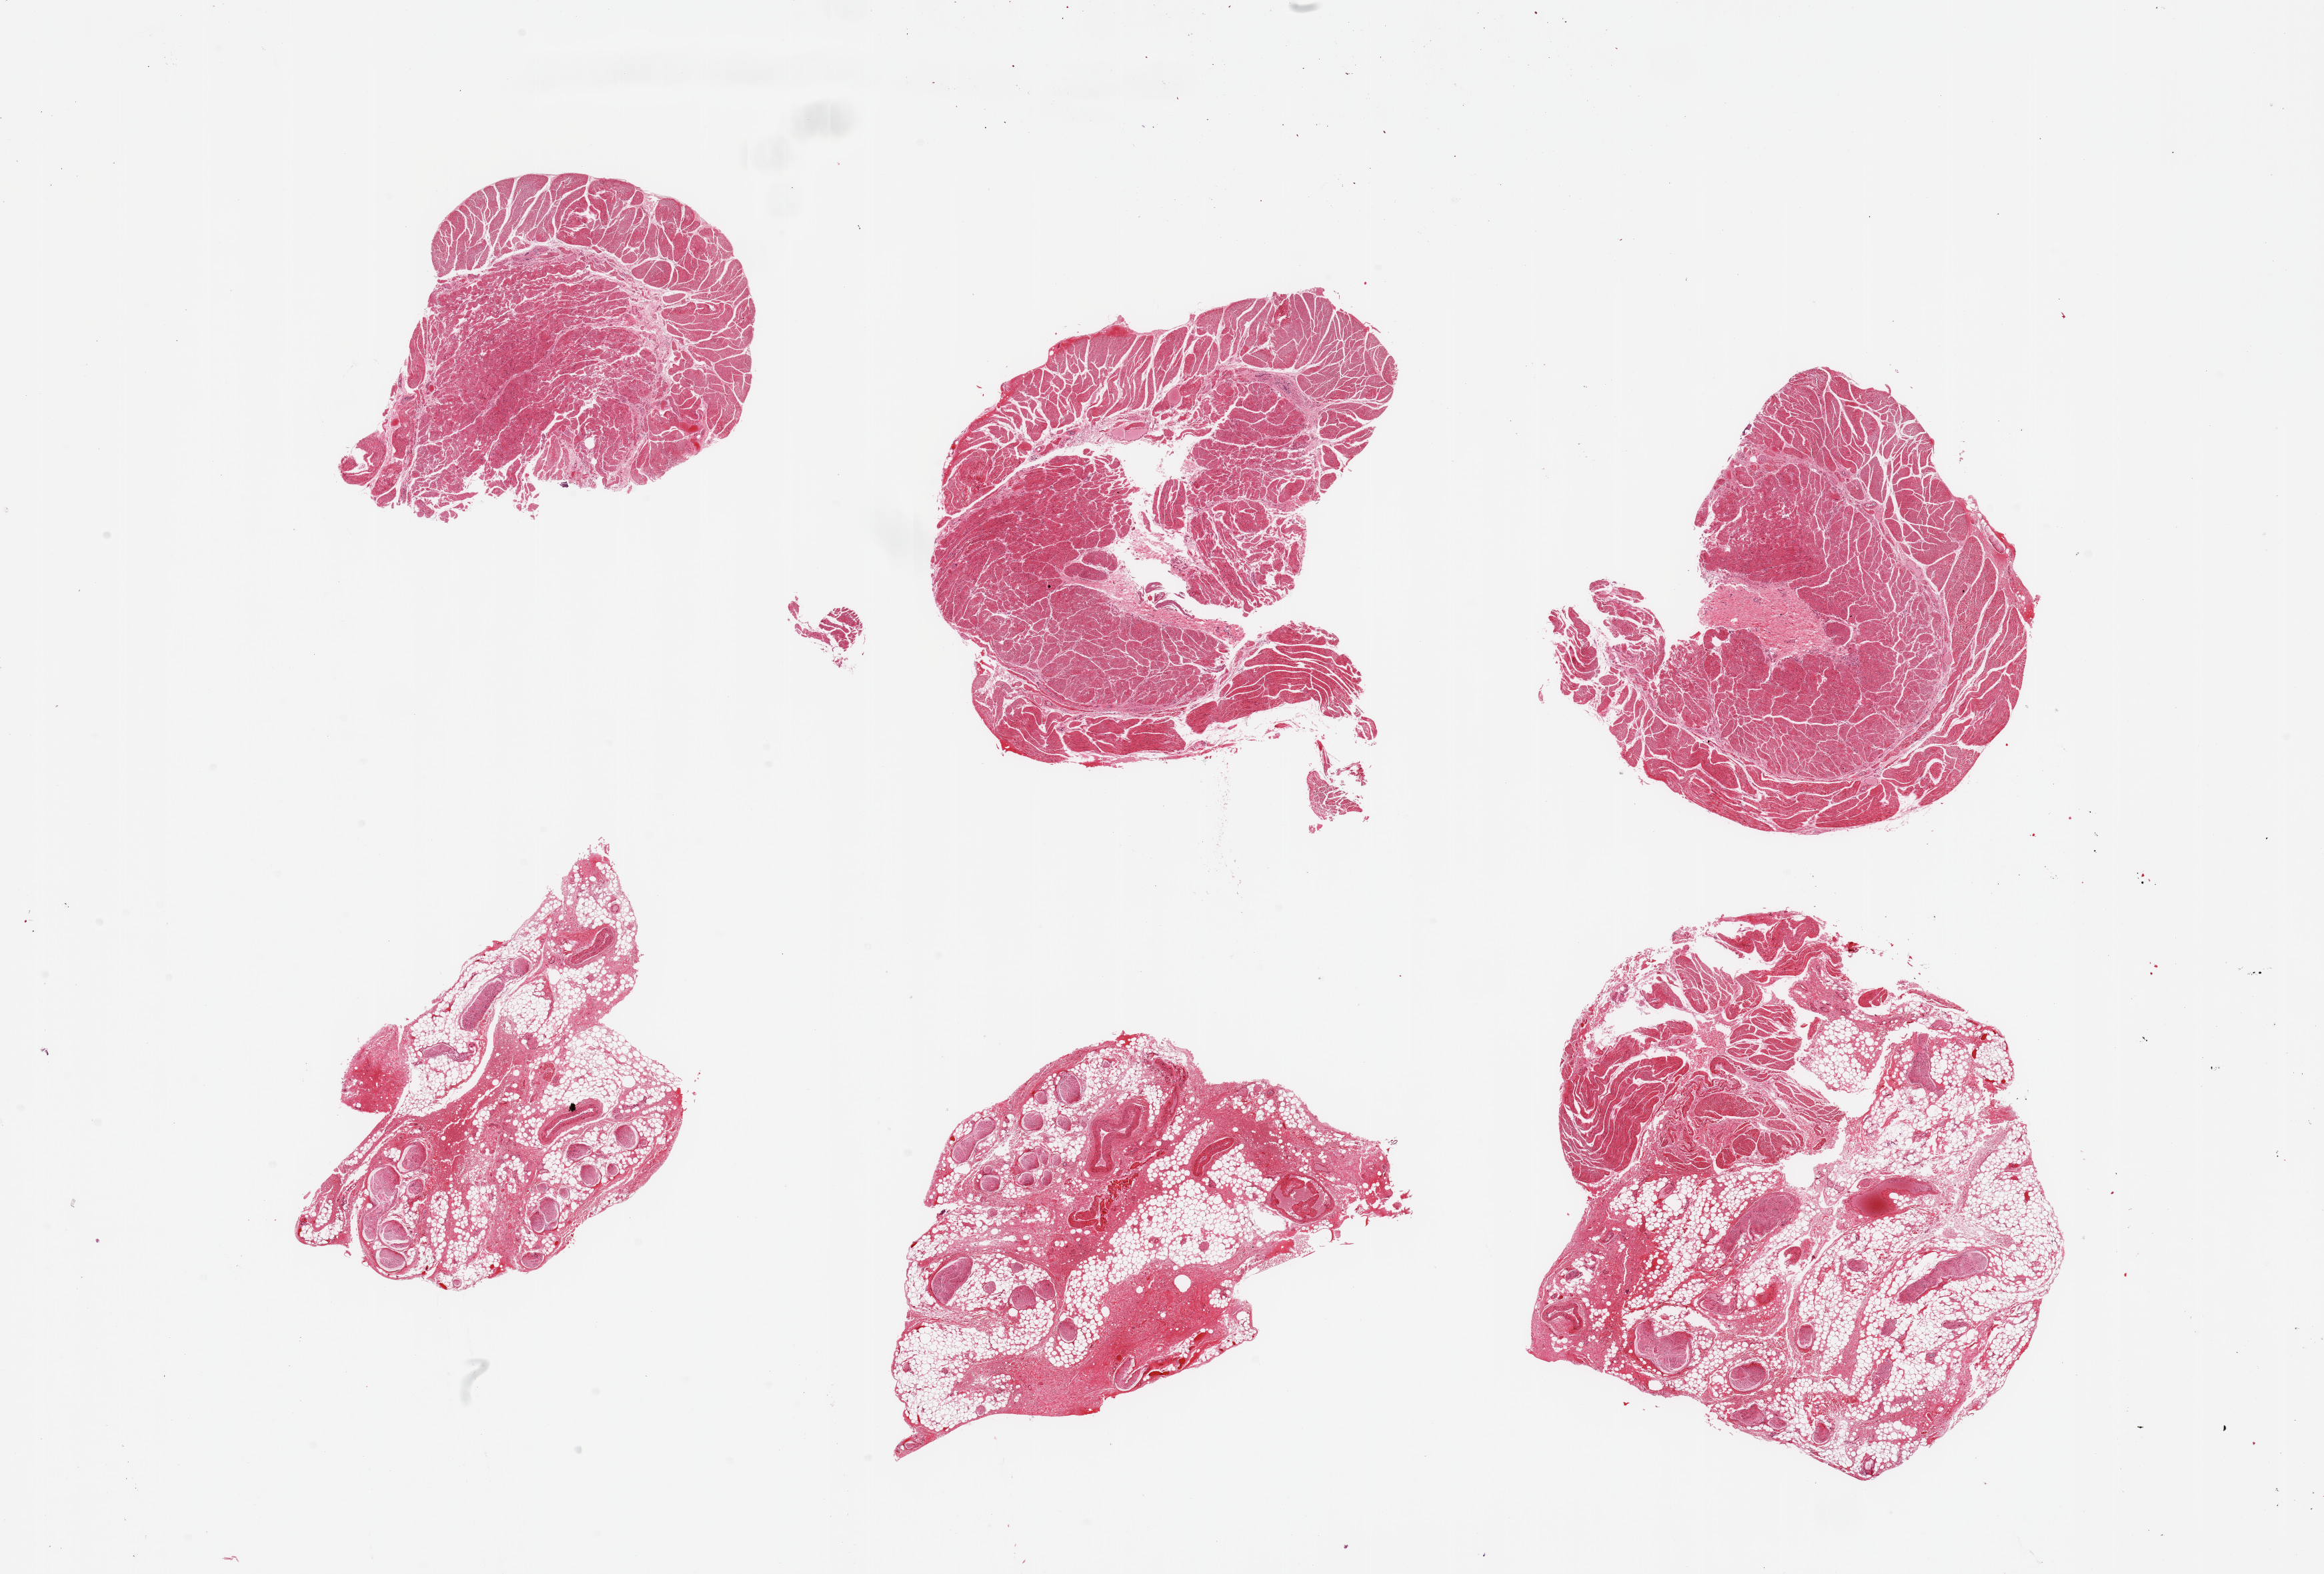
Digitized haematoxylin and eosin-stained section — whole scanned area (about 27.6 x 18.7 mm, from a 20x scan) shown as a low-resolution overview. PAXgene-fixed, paraffin-embedded tissue. Section of esophageal muscle (target tissue). Tissue donor sample. Donor sex: male.
* reviewer comment on this tissue sample: 6 pieces; 3 of 6 represent well trimmed muscularis